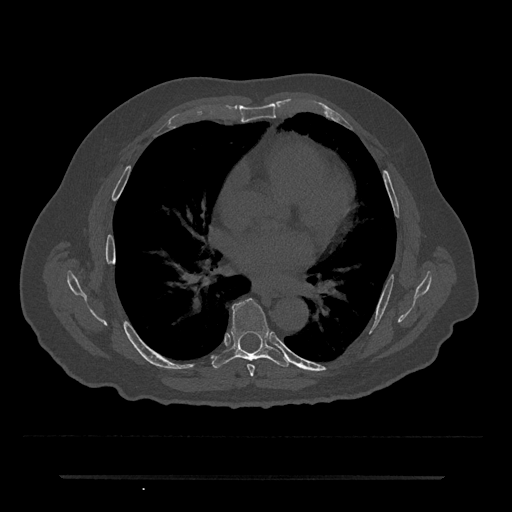
CT including the spine, one axial slice. Position 398 of 797 along the scan axis. 120 kVp. Bone window (W 1800 / L 400 HU). 512 × 512 image matrix, field of view 437 × 437 mm. Male patient, age 69 years. Case-level facts recorded for this patient, not image findings: primary cancer: prostate.
Annotated regions visible in this slice (semi-automatic segmentation, software-assisted and operator-edited):
- T6 vertebra: box from (x=247, y=364) to (x=255, y=376) px
- T7 vertebra: (x=212, y=298)–(x=290, y=369)